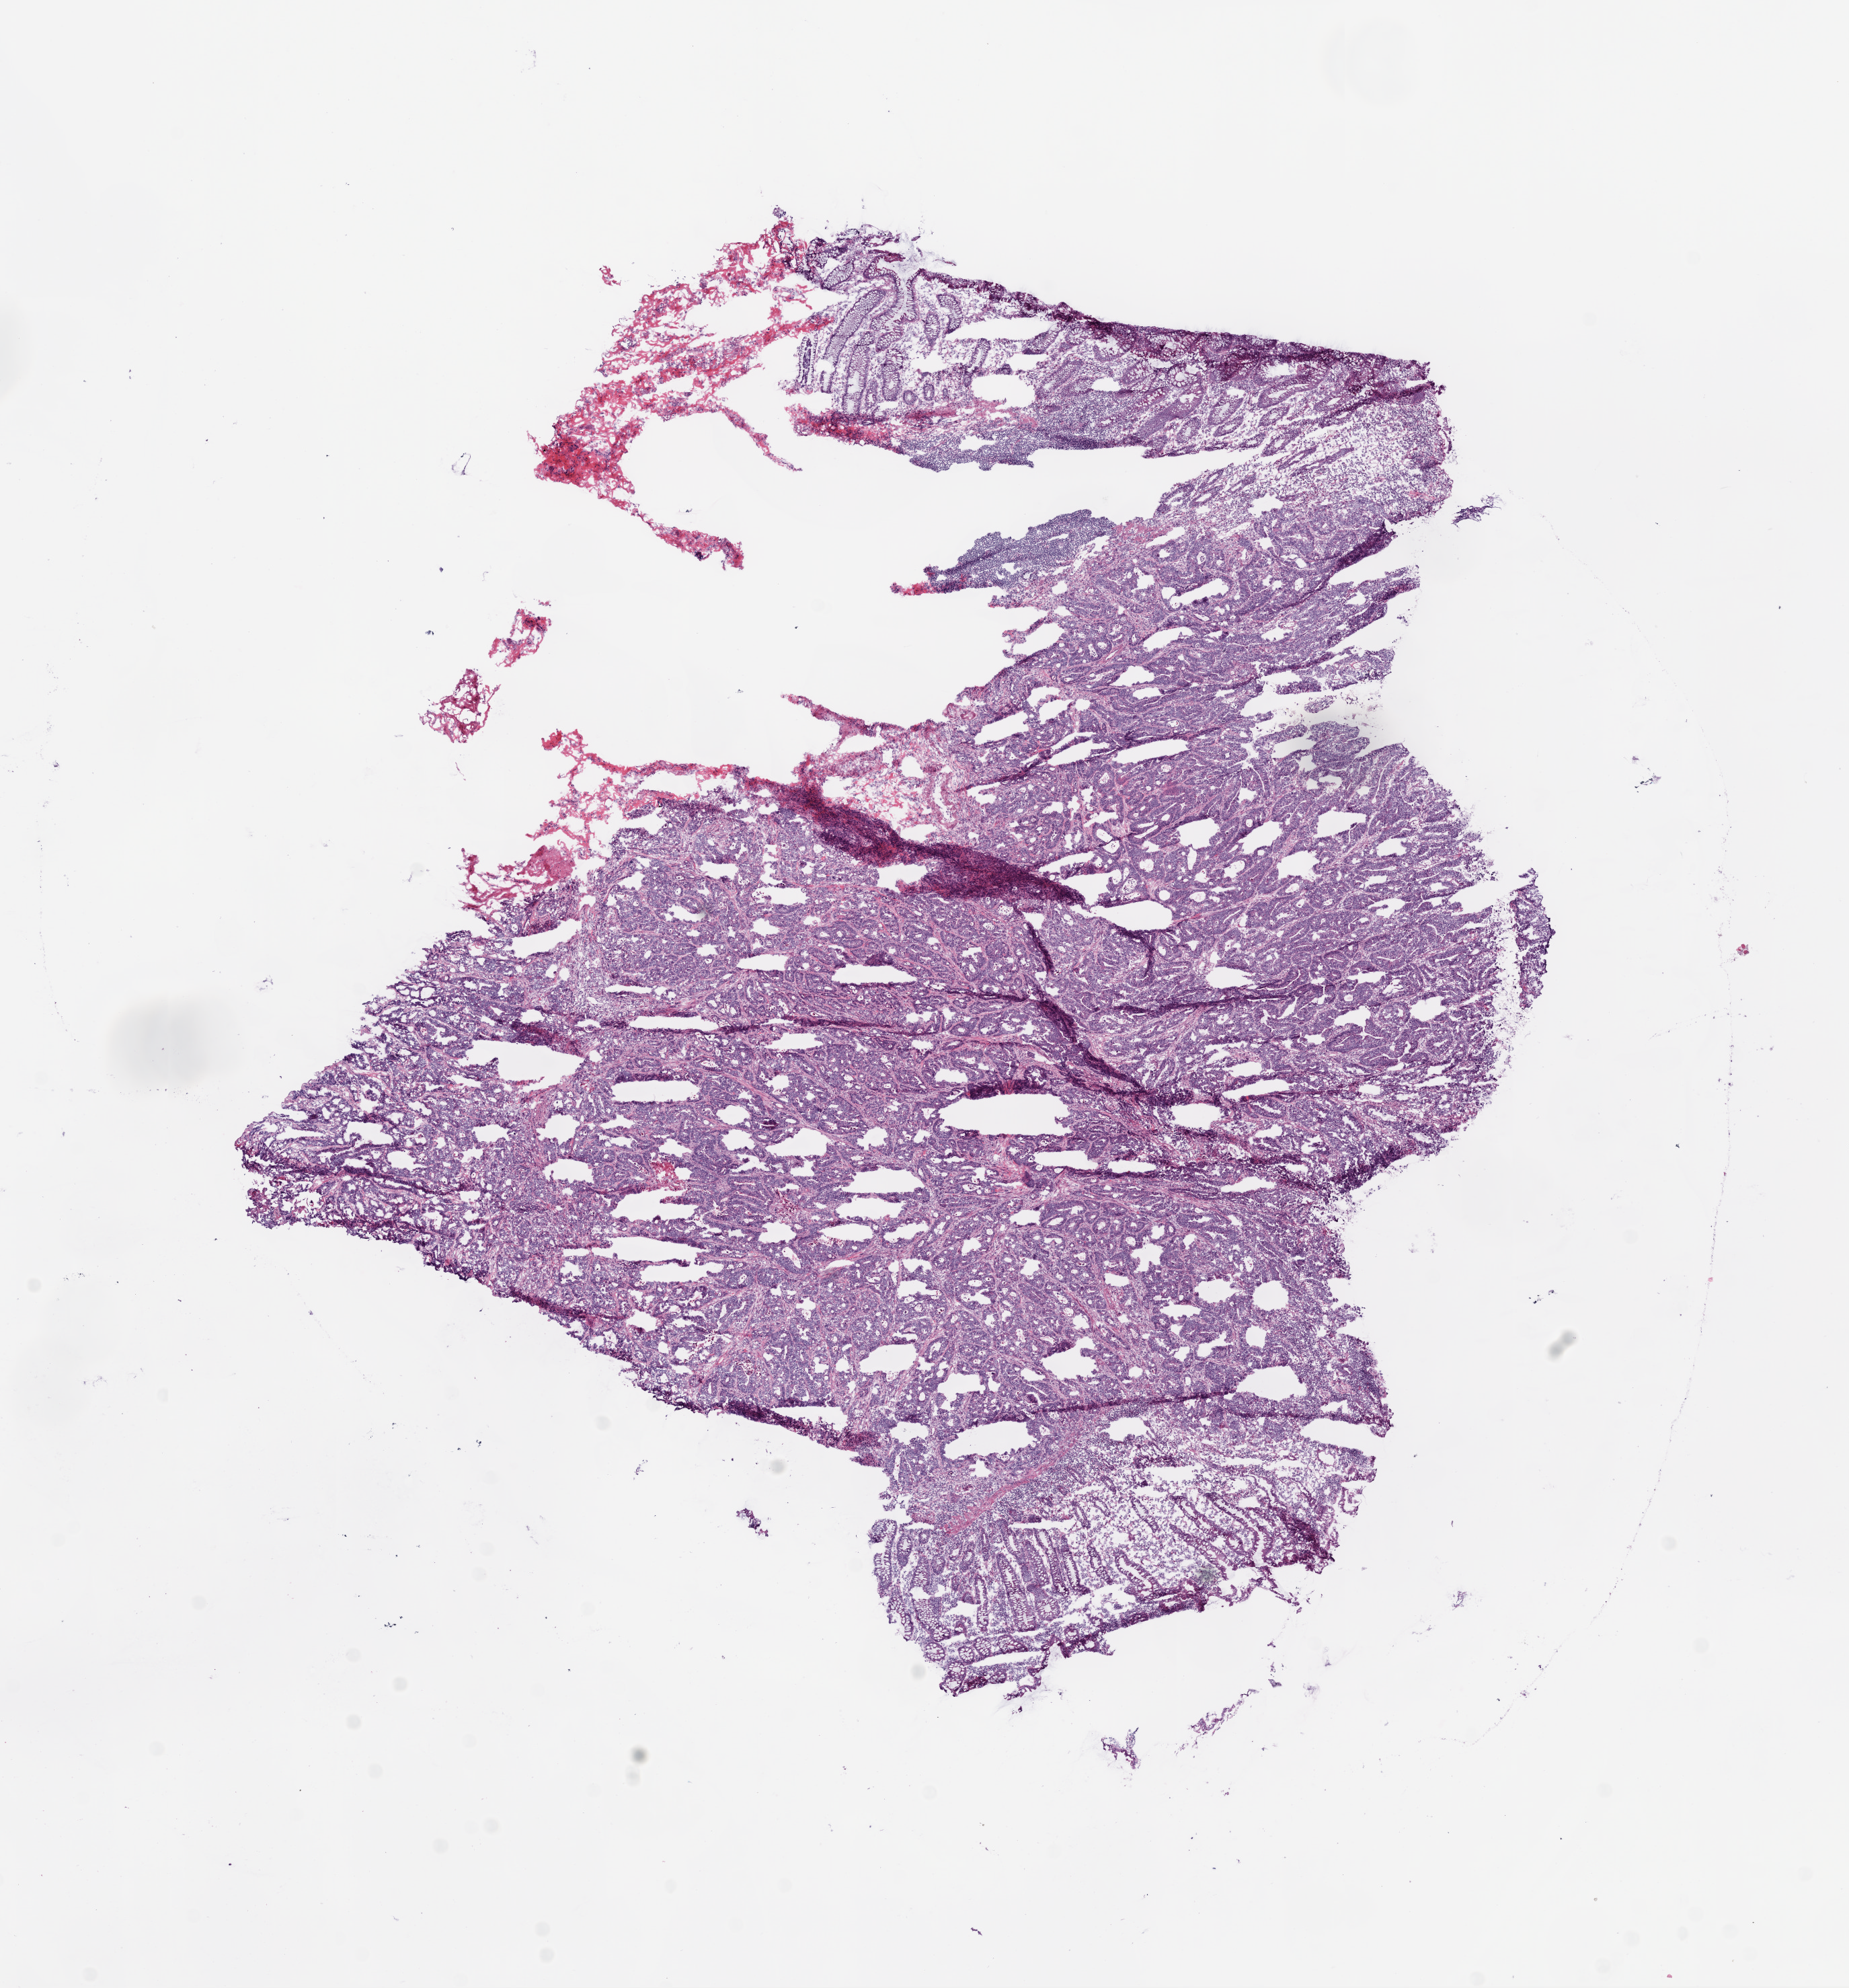
Digitized H&E tissue section (whole slide) — a low-resolution overview of the entire scanned area, about 11.0 x 11.9 mm (slide scanned at 20x), frozen section, sample: primary tumour, colon. Male, age 69 years at initial diagnosis. Slide review estimates, as recorded: tumour cells 80%, tumour nuclei 85%, normal cells 5%, stromal cells 15%, necrosis 0%.
AJCC pathologic stage: I. Lymph nodes positive (case pathology): 0 of 31 examined. TNM: T2 N0 M0. Diagnosis: Adenocarcinoma, NOS.